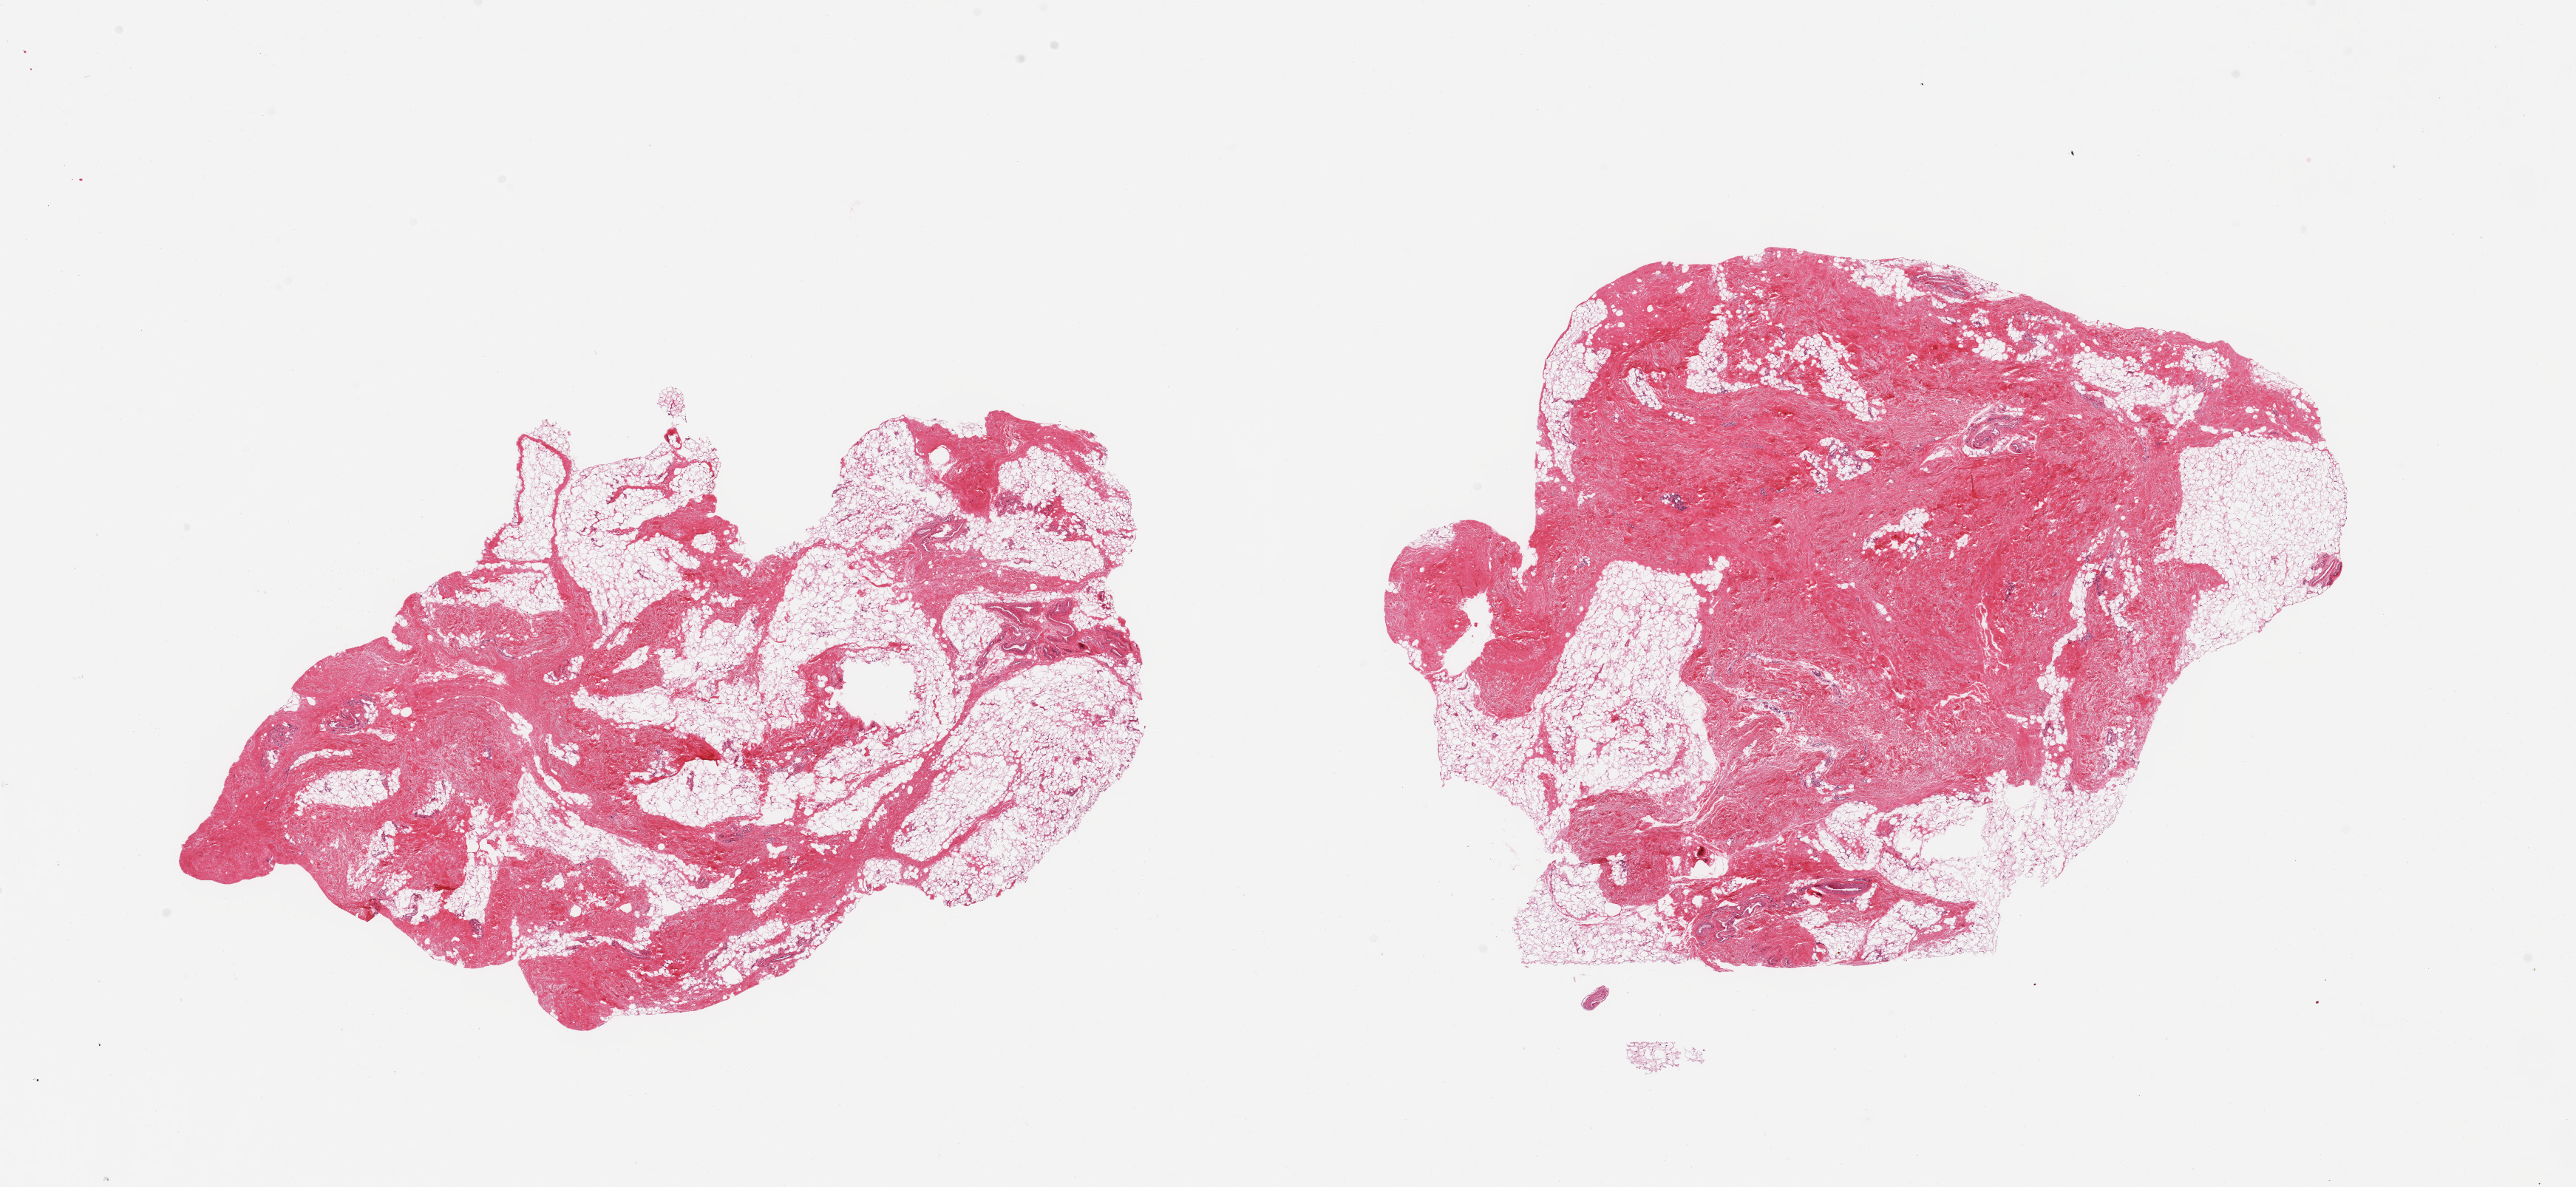
Whole-slide image, hematoxylin and eosin (H&E) stain, brightfield — whole scanned area (about 27.6 x 12.7 mm) shown as a low-resolution overview, PAXgene-fixed, paraffin-embedded tissue, section of breast (target tissue), donor tissue sample. Donor sex: male.
* reviewer comment on this tissue sample: 22 pieces; fibrofatty tissue without mammary ducts